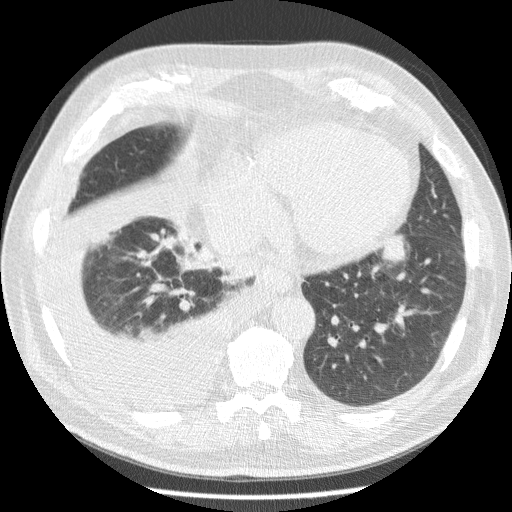
Low-dose screening chest CT, one axial slice. Slice 63 of 180 in the series (ordered by position). Reconstruction kernel STANDARD. 120 kVp. Lung window (W 1500 / L -600 HU). 2.5 mm slice thickness. 512 × 512 image matrix, field of view 355 × 355 mm.
Annotated regions visible in this slice (manually delineated by an expert):
- lesion 1 (tumor, lower lobe of left lung): bounding box (x1, y1, x2, y2) in pixels: (381, 235, 405, 266)